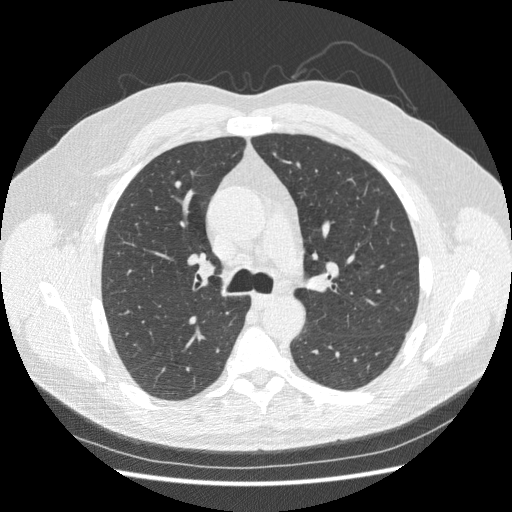
Low-dose screening chest CT, one axial slice; slice 158 of 250 in the series (ordered by position); reconstruction kernel STANDARD; 120 kVp; lung window (W 1500 / L -600 HU); 1.25 mm slice thickness; 512 × 512 image matrix.
Structures marked on this image (manually delineated by an expert):
- lesion 1 (tumor, upper lobe of right lung): bounding box <175,180,182,188> (left, top, right, bottom; pixels)